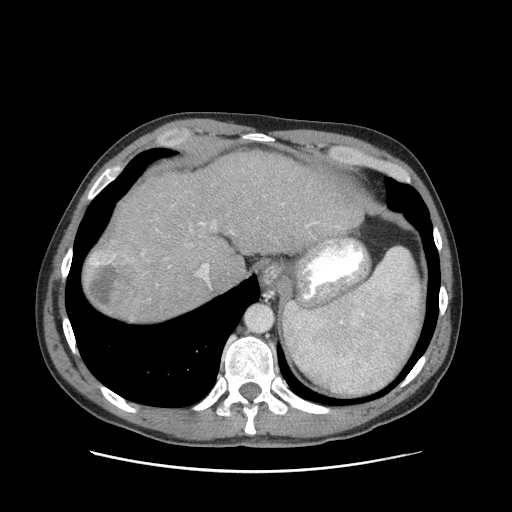
Contrast-enhanced abdominal CT (liver protocol), one axial slice. Position 78 of 93 along the scan axis. Reconstruction kernel STANDARD. 120 kVp. Soft-tissue window (W 400 / L 40 HU). 2.5 mm slice thickness. 512 × 512 image matrix, field of view 380 × 380 mm. Case-level facts recorded for this patient, not image findings: diagnosis: hepatocellular carcinoma (patient treated with transarterial chemoembolisation; whether this scan precedes or follows treatment is not stated here); TNM stage (as recorded): Stage-II; Child-Pugh class: A; tumour differentiation: moderately differentiated; tumour size: 1 cm.
Annotated regions visible in this slice (semi-automatic segmentation, software-assisted and operator-edited):
- abdominal aorta: bounding box <245,305,272,331> (left, top, right, bottom; pixels)
- liver parenchyma outside the tumour (the mass and vessels are separate outlines, so this box may not span the whole liver): <82,150,369,322>
- mass: <87,248,143,317>
- liver vessels: <169,222,209,281>